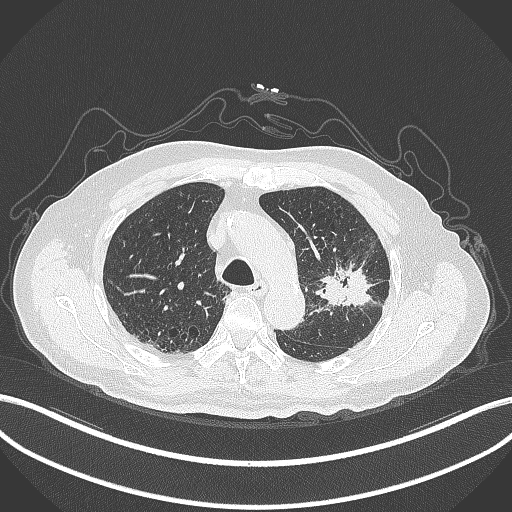
Chest CT, one axial slice. Position 214 of 331 along the scan axis. Reconstruction kernel B70f. Lung window (W 1500 / L -600 HU). 1 mm slice thickness. 512 × 512 image matrix, field of view 400 × 400 mm. Male patient, age 79 years. Case-level facts recorded for this patient, not image findings: clinical TNM (as recorded): T2a N1 M1; histopathological grade: G3.
Annotated regions visible in this slice (bounding box drawn by a radiologist):
- lung tumour (recorded histology: adenocarcinoma): bounding box (x1, y1, x2, y2) in pixels: (310, 246, 384, 312)